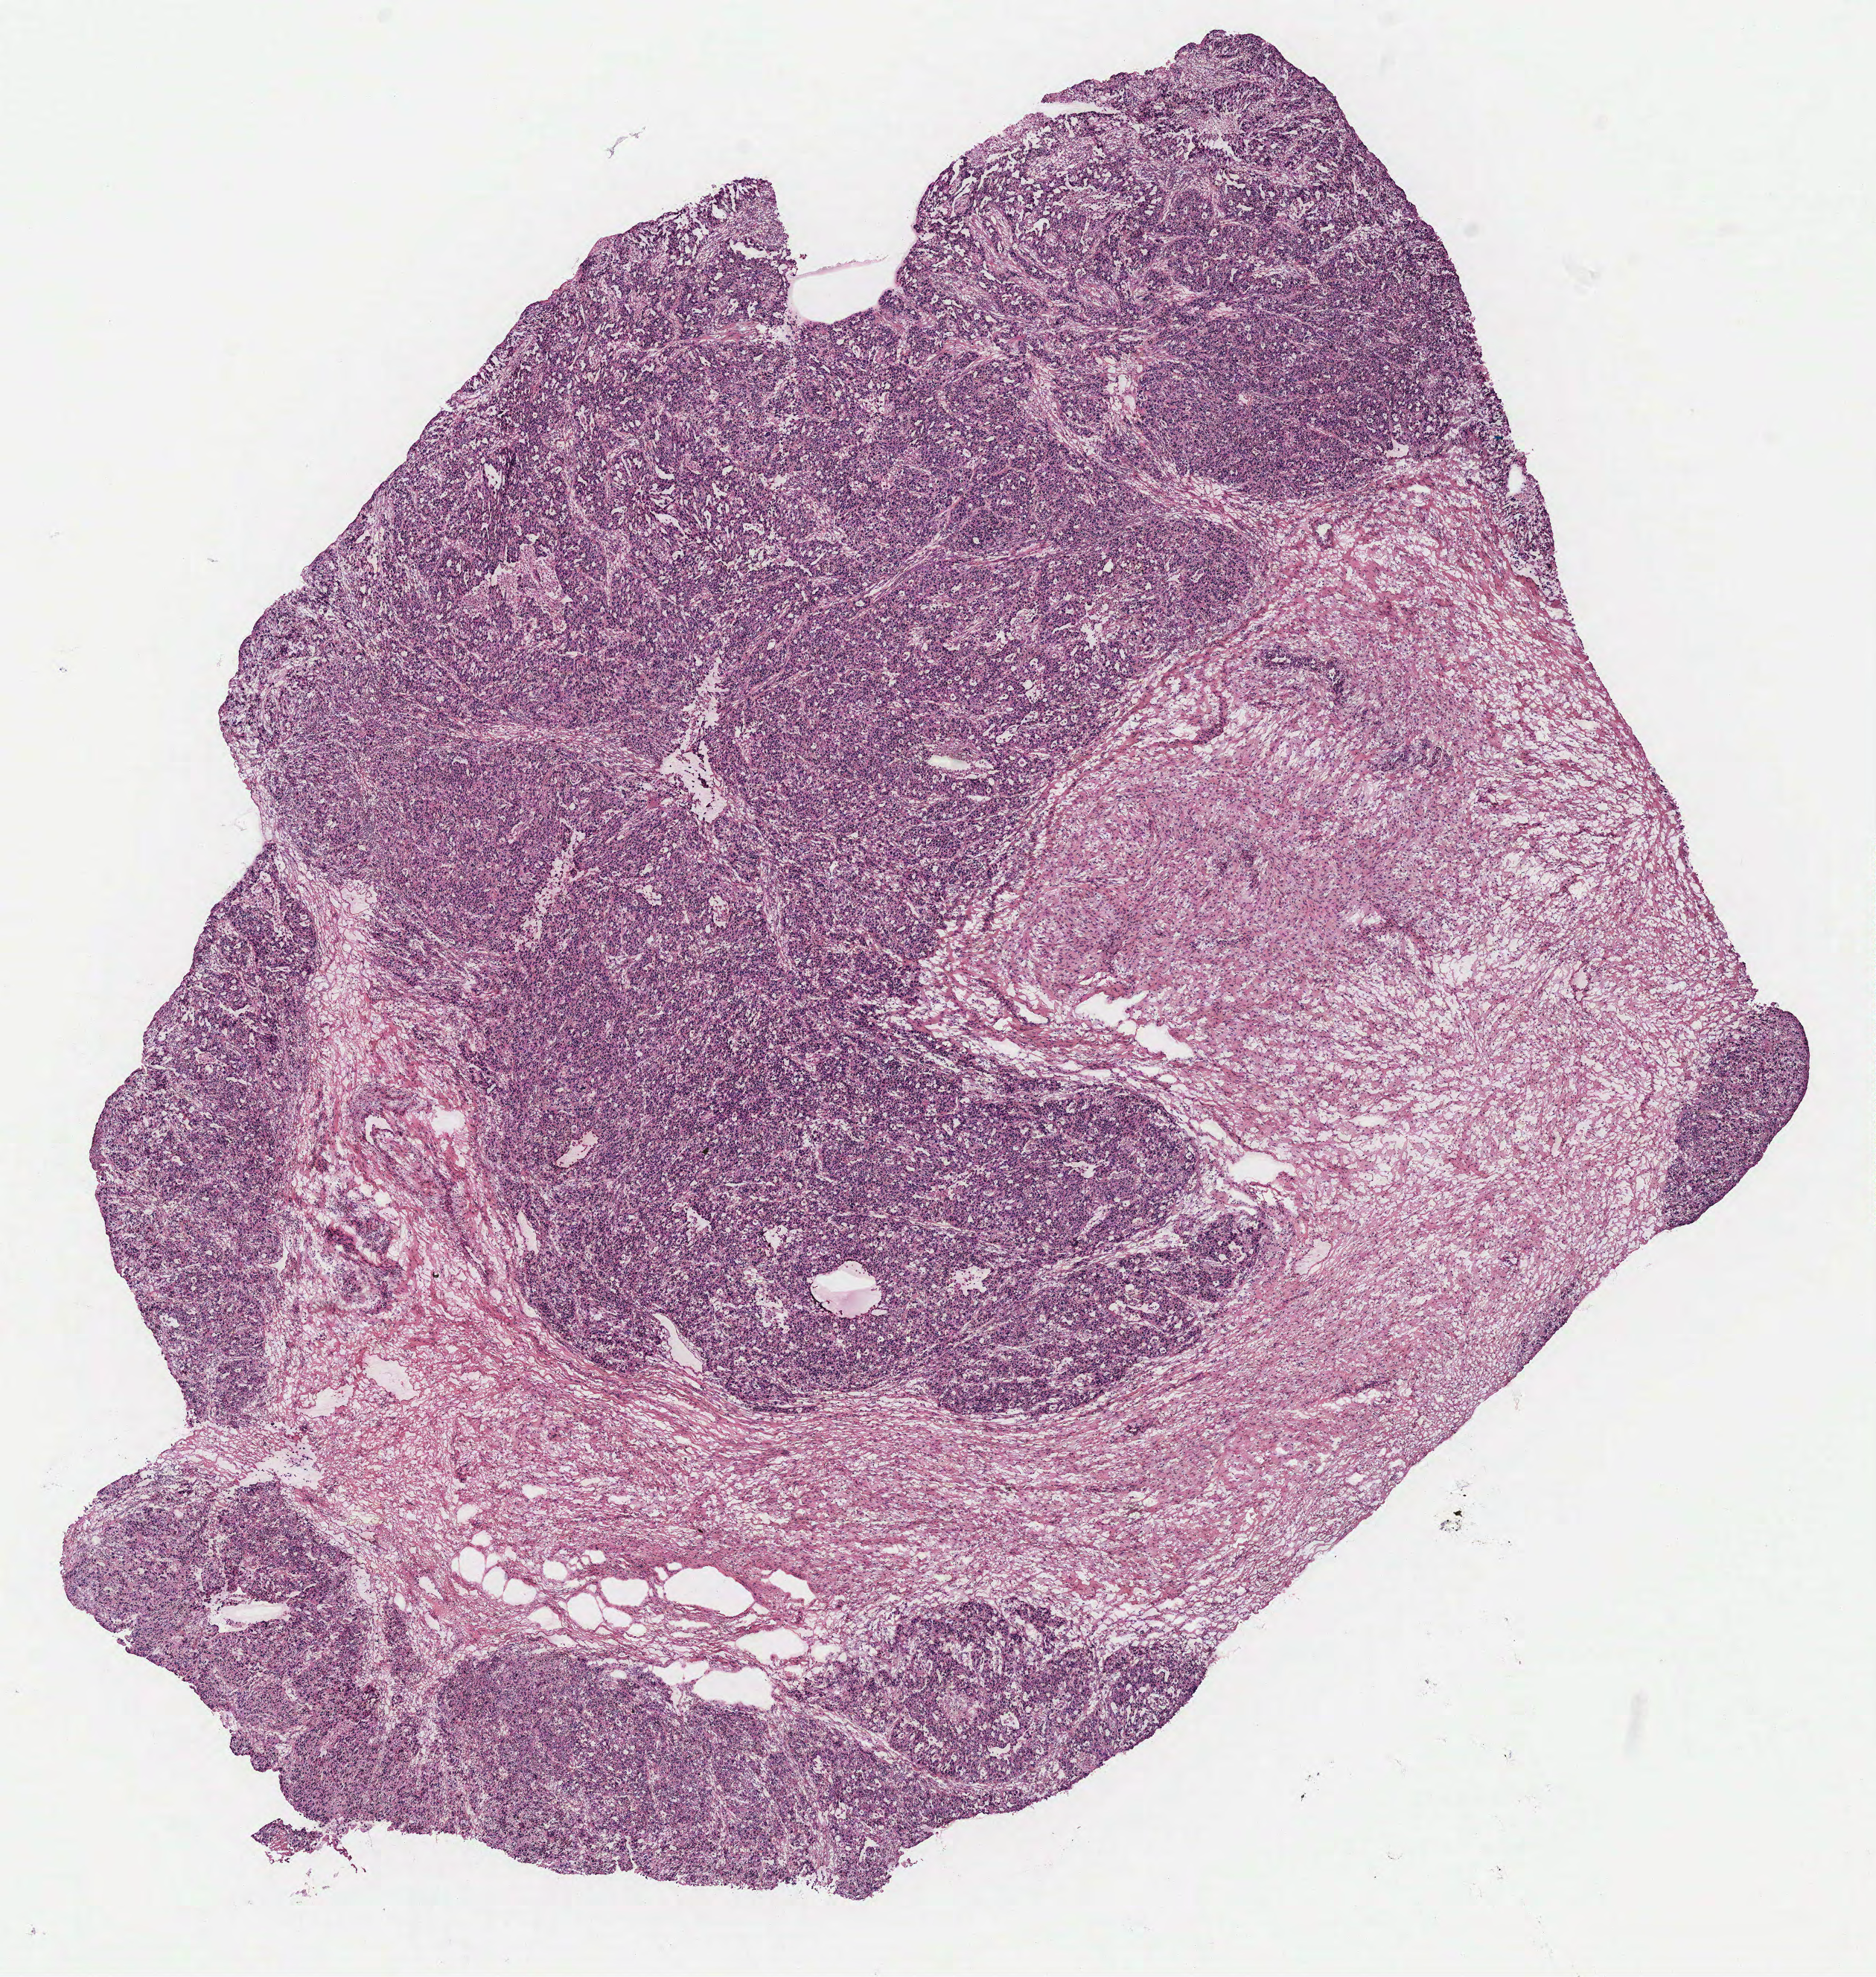
H&E whole-slide image, shown as a low-resolution overview of the whole scanned area (about 10.1 x 10.6 mm, from a 40x scan), ovary, tumour tissue. Female, 52 y/o.
Diagnosis: Serous adenocarcinoma, NOS (fallopian tube).